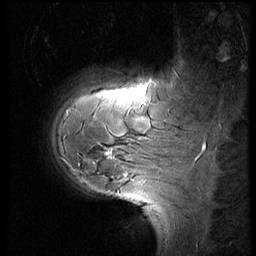
Breast MRI (dynamic contrast-enhanced), one sagittal slice. 3 images stored at this slice position (order not interpretable as contrast timing). 1.5 T. TE 4.2 ms, TR 8.9 ms. 2.5 mm slice thickness. 256 × 256 image matrix, field of view 200 × 200 mm. Female patient, age 29 years. Case-level facts recorded for this patient, not image findings: setting: breast cancer imaged before/during neoadjuvant chemotherapy.
Structures marked on this image (semi-automatically segmented with operator editing):
- analysis volume of interest (the breast-tissue region the enhancement analysis was run in; not a lesion): bounding box [x1, y1, x2, y2] px = [52, 57, 185, 200]
- tumour enhancement mask (voxels above the 140 % enhancement threshold inside the analysis volume of interest): [108, 153, 112, 157]